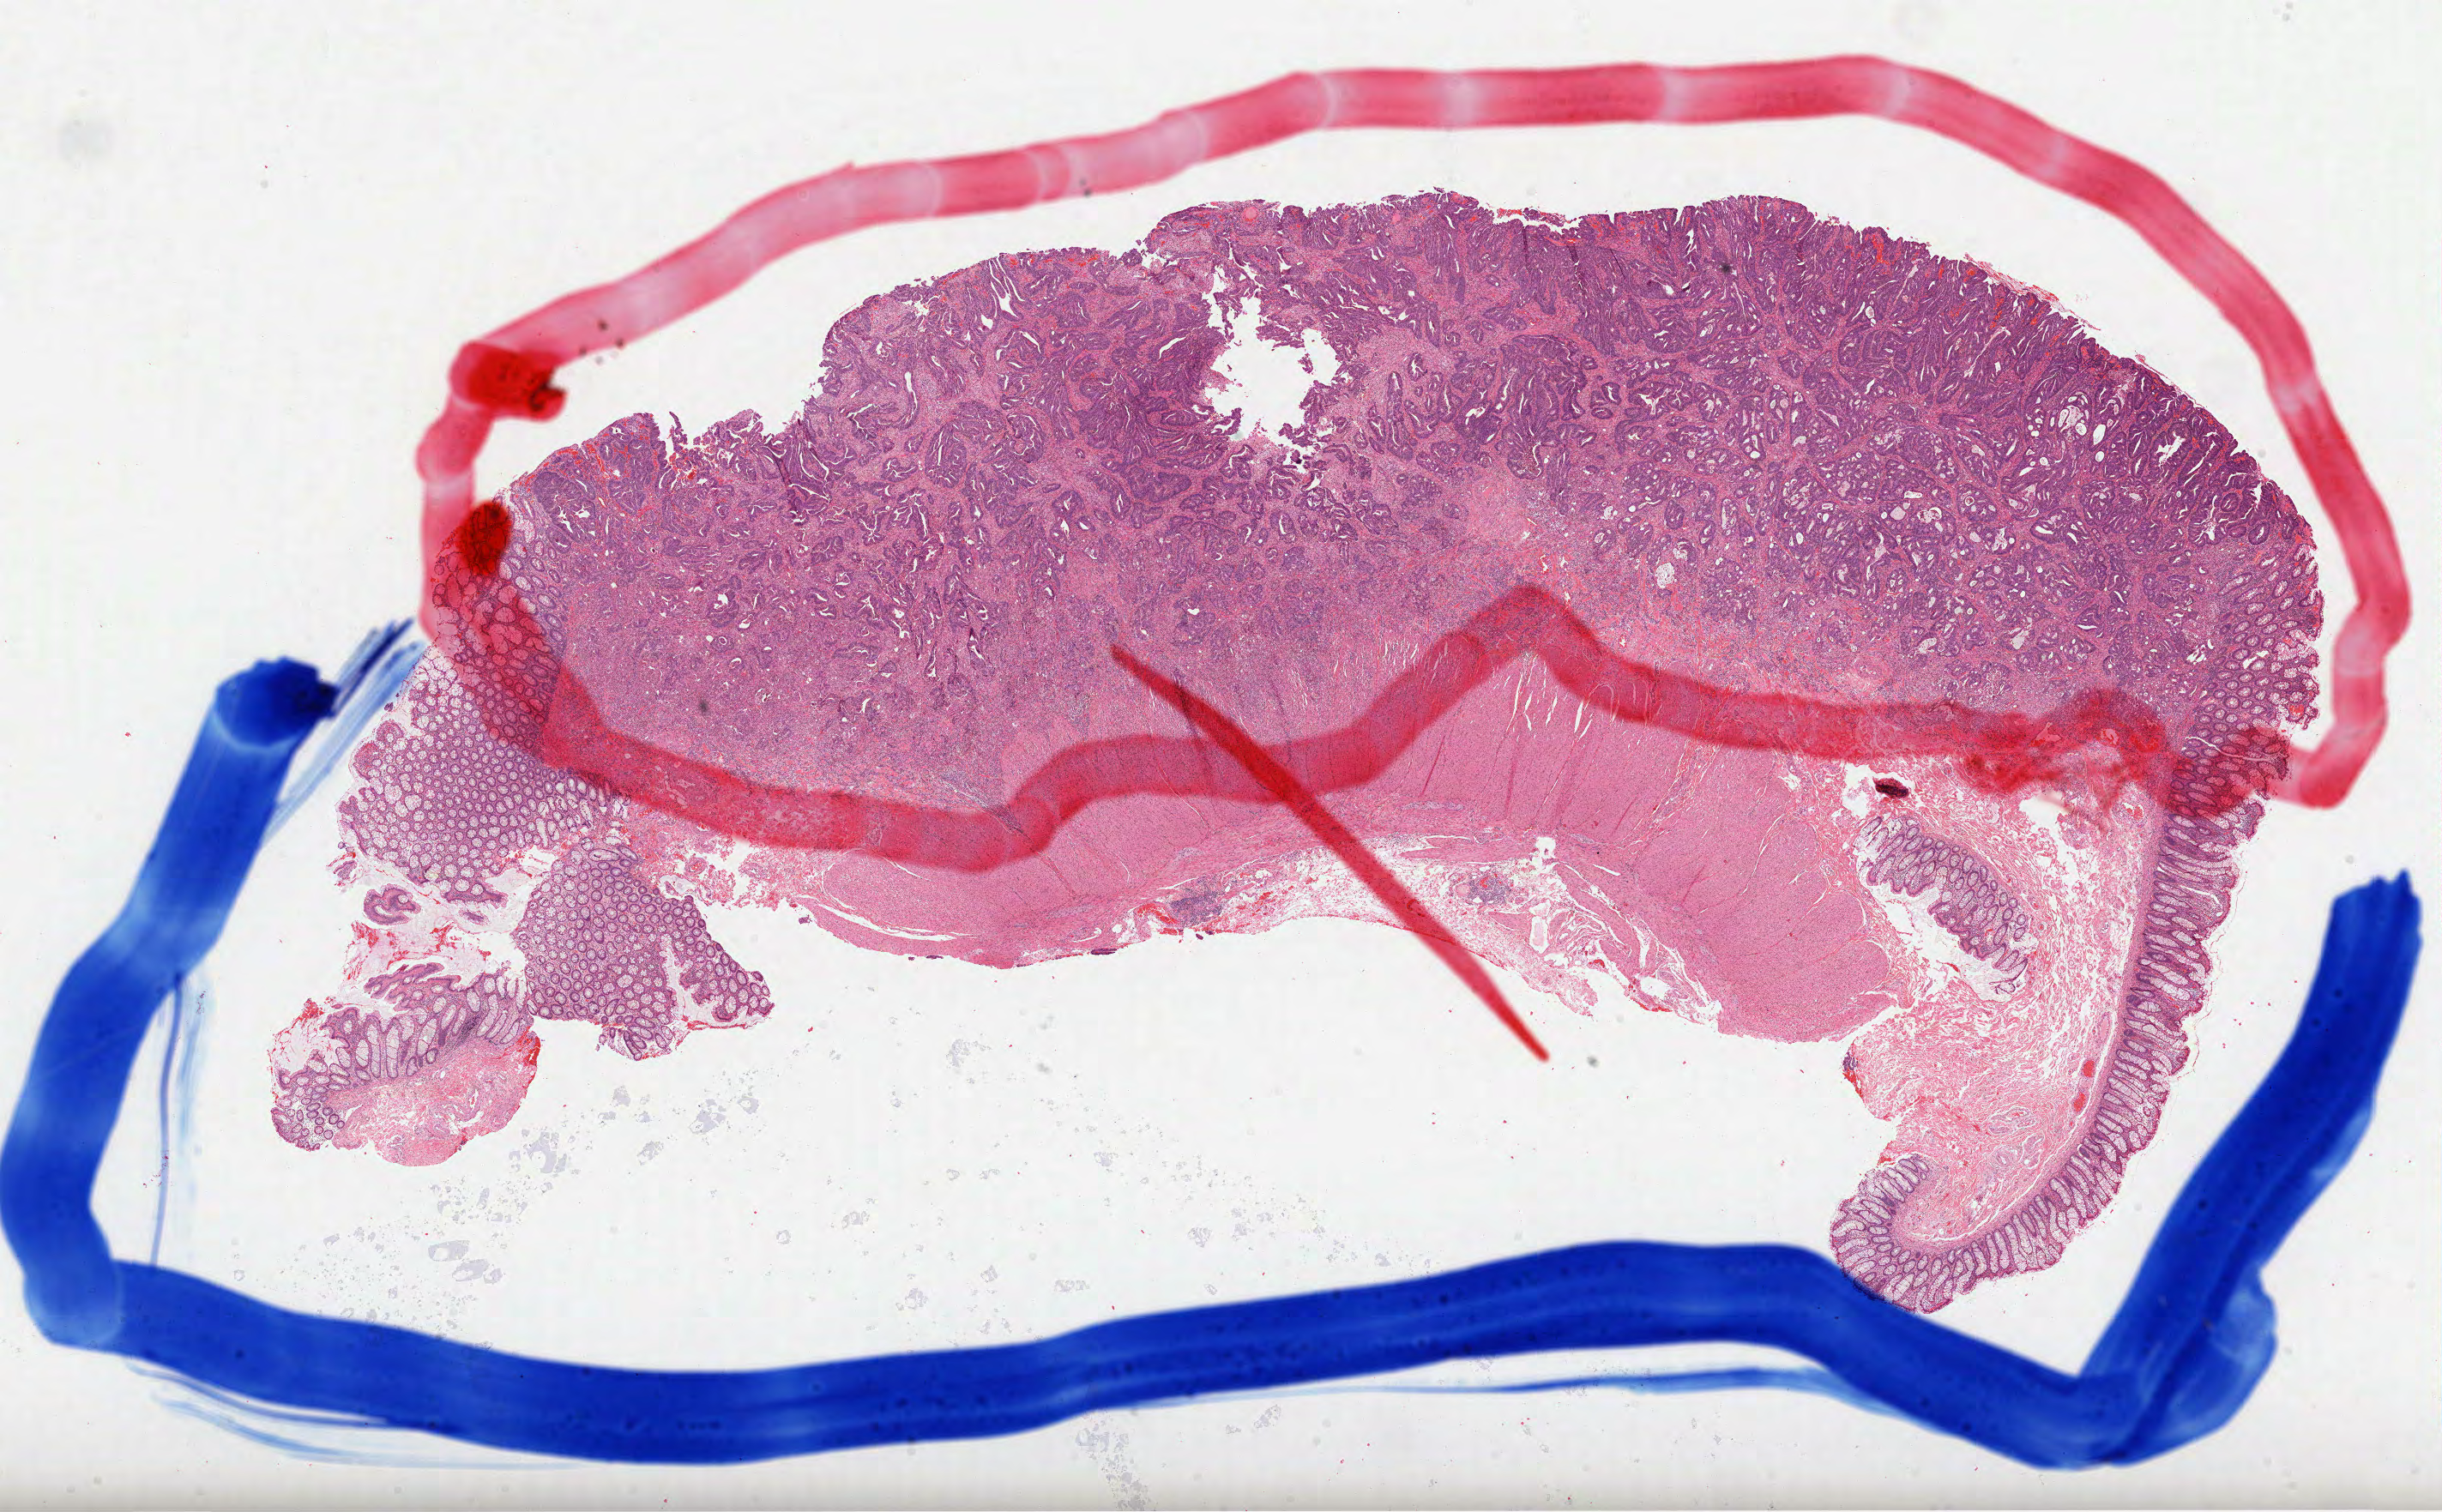
H&E-stained whole-slide image — whole scanned area (about 23.0 x 14.2 mm, slide scanned at 40x) shown as a low-resolution overview. FFPE section. Colon, primary tumour sample. Patient: female, age at initial diagnosis 58 years.
- pathologic diagnosis: Adenocarcinoma, NOS
- AJCC pathologic stage: IIA (7th edition)